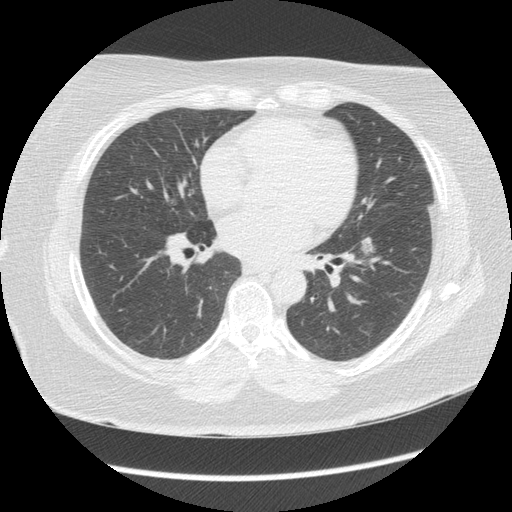
Low-dose screening chest CT, axial slice, third screening round (two years after baseline), lung window (W 1500 / L -600 HU), slice 79 of 144 in the series, 512 × 512 image matrix, field of view 360 × 360 mm. Female participant, aged 65 years at enrolment.
Expert-annotated lung lesion, box from (x=349, y=230) to (x=379, y=267) px. Reader record for this screening exam (exam-level; its link to the box is not recorded): non-calcified nodule or mass ≥4 mm, left lower lobe, 130 × 90 mm, poorly defined margins, mixed attenuation, pre-existing on the prior screen: yes; interval growth: yes. Lung cancer was diagnosed 35 days after this screen: adenocarcinoma, NOS, left lower lobe, moderately differentiated (G2), stage IA (AJCC 6th edition), 12 mm at pathology.